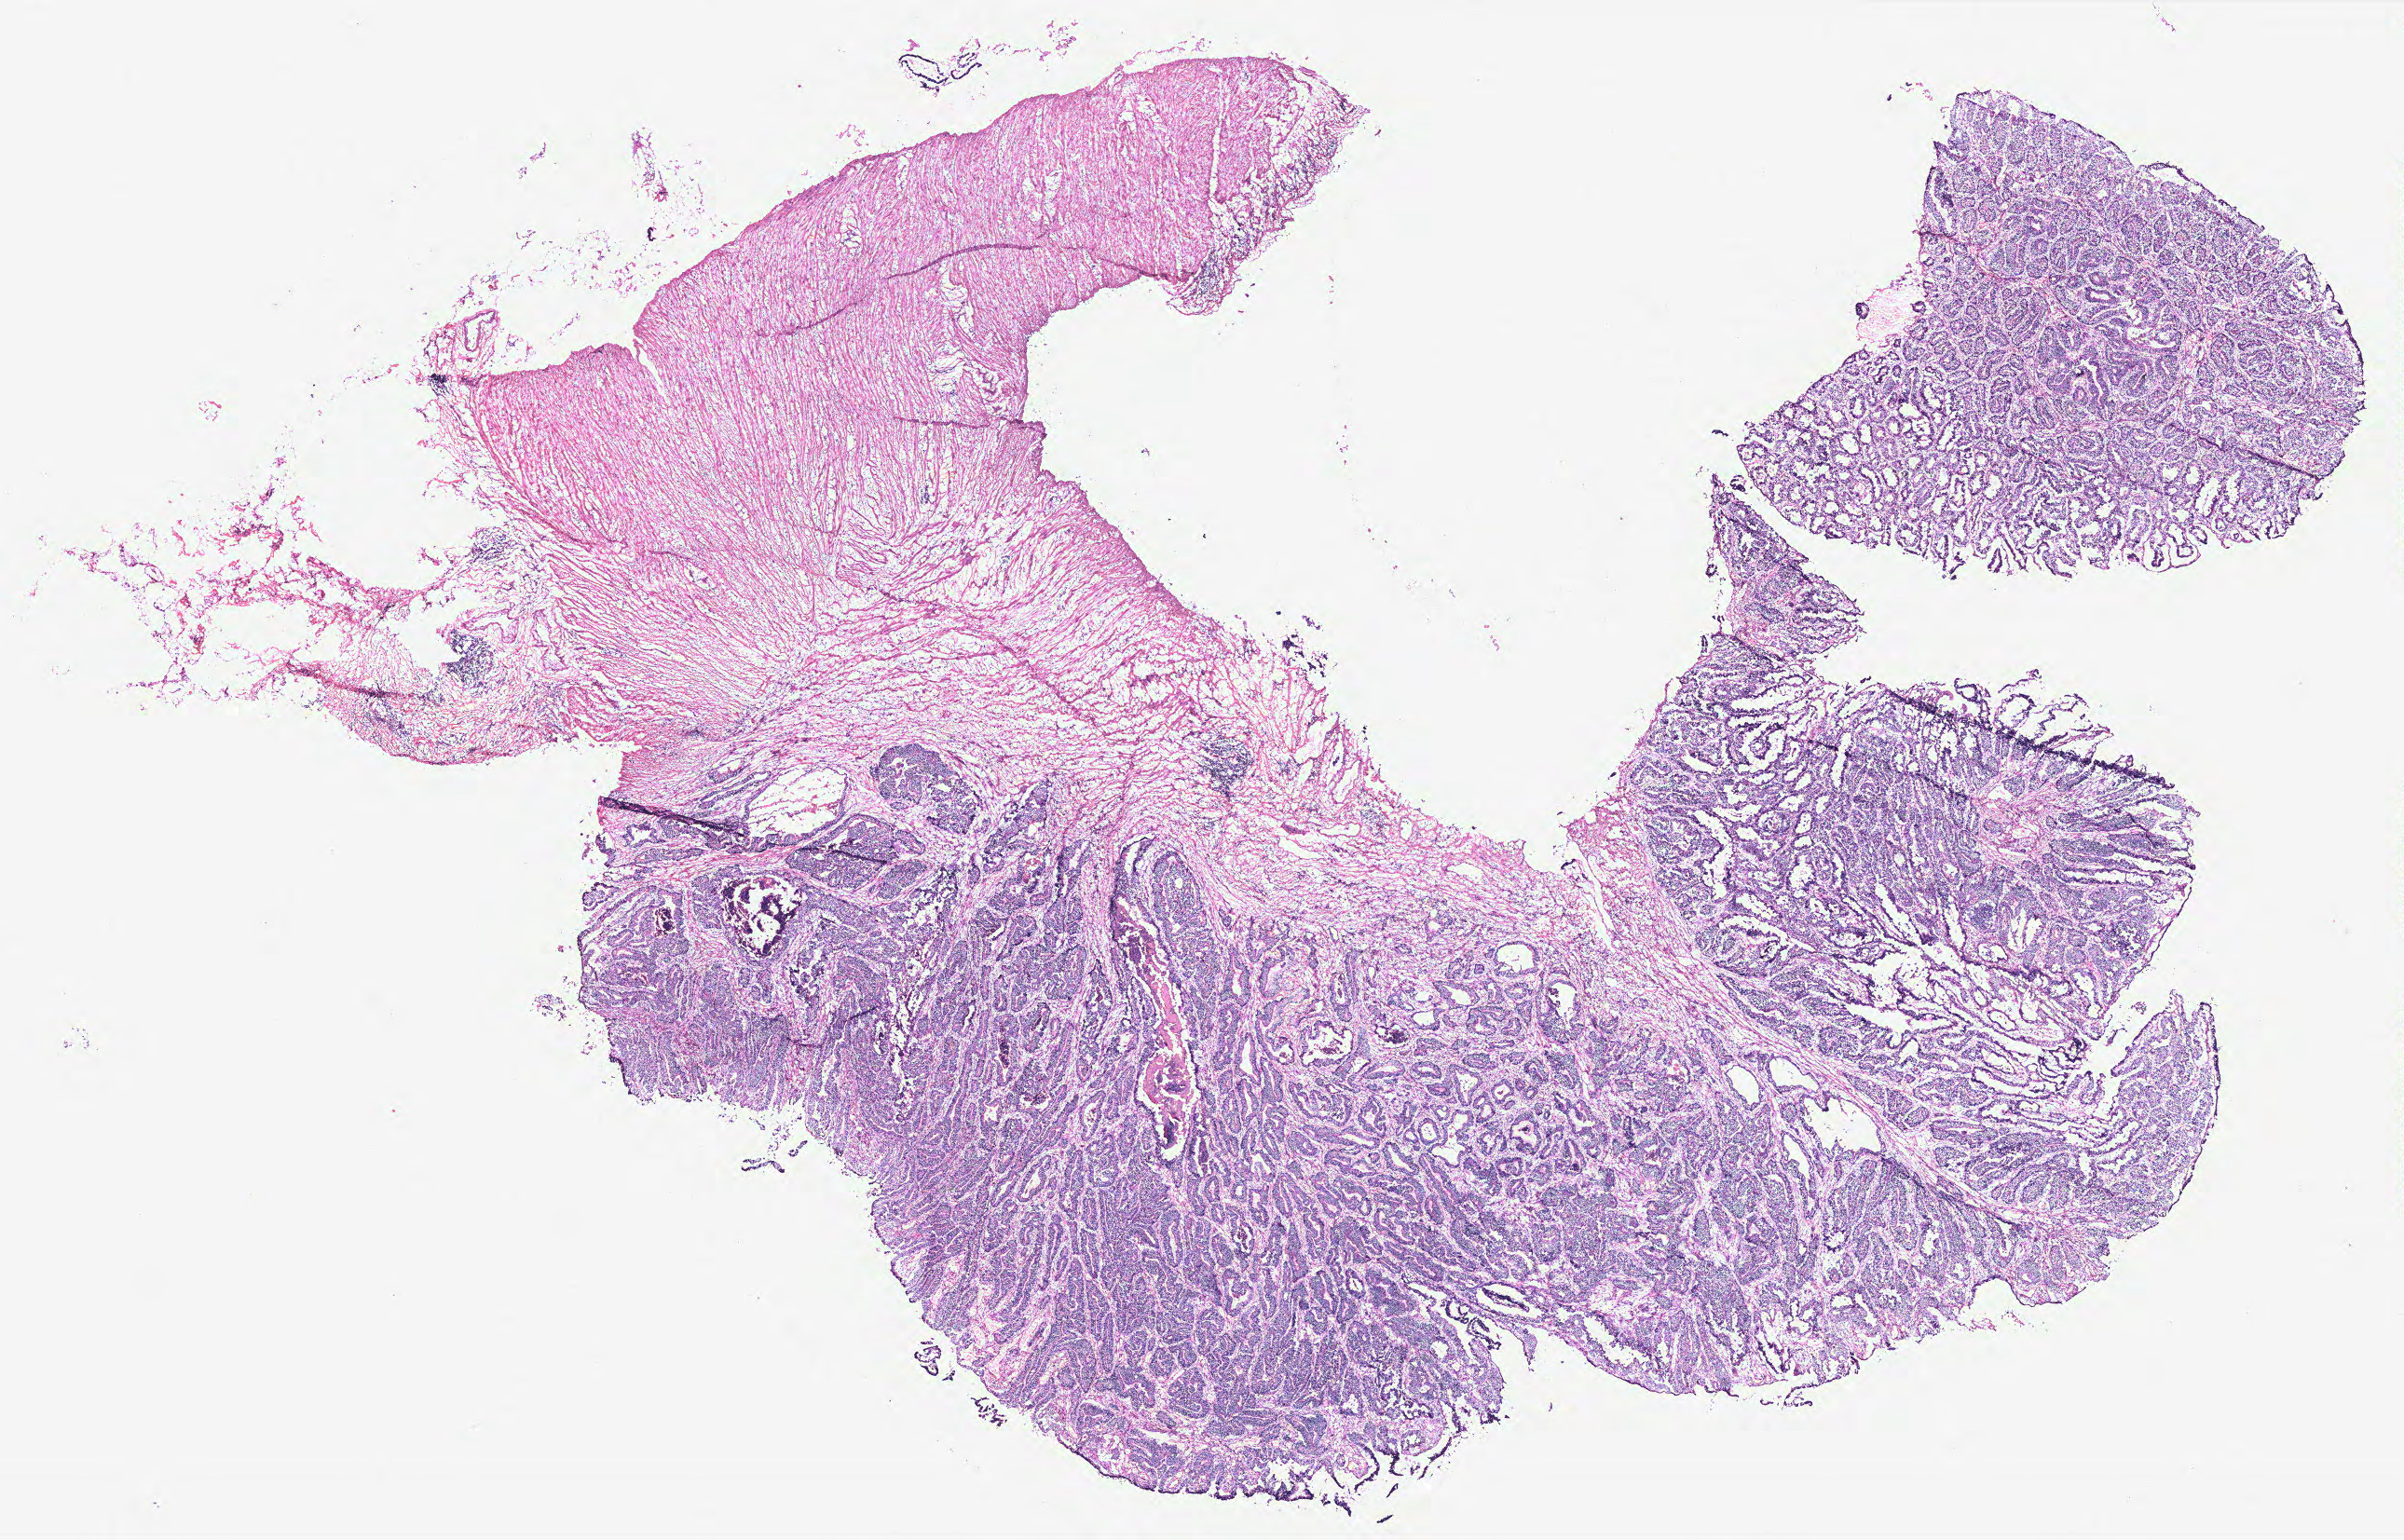
Digitized H&E-stained tissue section (whole slide), whole scanned area (about 20.6 x 13.2 mm) shown as a low-resolution overview, tumour tissue sample, colon. Female, 55 y/o.
Diagnosis: Adenocarcinoma, NOS. Primary tumour site (as recorded): colon. AJCC pathologic stage: IIA.